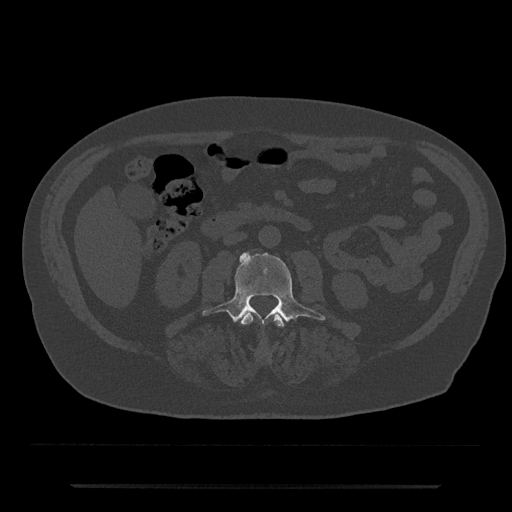
CT including the spine, one axial slice; slice 422 of 797 in the series (ordered by position); reconstruction kernel Br40s/3; 120 kVp; bone window (W 1800 / L 400 HU); 0.5 mm slice thickness; 512 × 512 image matrix, field of view 434 × 434 mm. Male patient, age 80 years. Case-level facts recorded for this patient, not image findings: primary cancer: prostate; vertebrae with lytic lesions (as recorded): L1, T11.
Outlined on this slice (semi-automatic segmentation, software-assisted and operator-edited):
- L2 vertebra: box from (x=241, y=312) to (x=284, y=327) px
- L3 vertebra: (x=202, y=252)–(x=325, y=324)